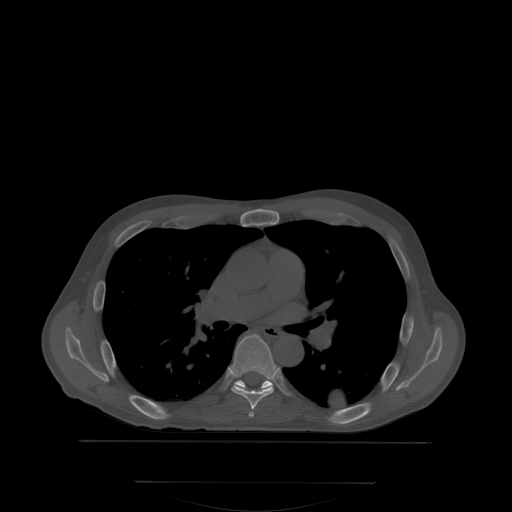
CT including the spine, one axial slice; position 234 of 350 along the scan axis; bone window (W 1800 / L 400 HU); 2.5 mm slice thickness; 512 × 512 image matrix, field of view 500 × 500 mm. Male patient, age 58 years. From the clinical record (not read from this slice): primary cancer: prostate.
Annotated regions visible in this slice (semi-automatically segmented with operator editing):
- T6 vertebra: box from (x=229, y=335) to (x=276, y=416) px
- T7 vertebra: (x=233, y=378)–(x=273, y=391)